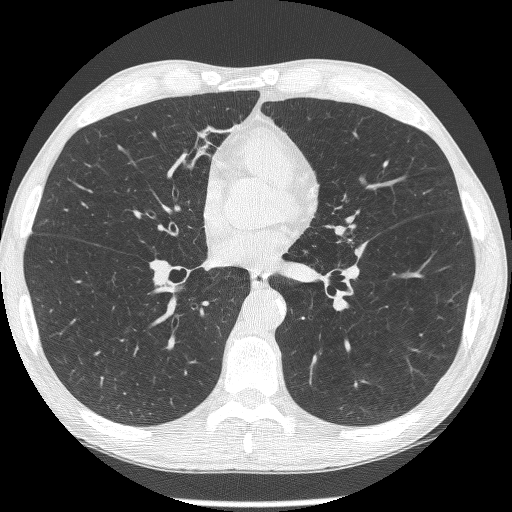
Axial slice from a low-dose chest CT screening exam, second annual screen, lung window (W 1500 / L -600 HU), 1.25 mm slice thickness, 120 kVp, slice 129 of 293 in the series. Male participant, aged 62 years at enrolment. Former smoker at enrolment.
Expert-annotated lung lesion, box from (x=322, y=216) to (x=370, y=264) px. The screening reader recorded 2 non-calcified nodules or masses ≥4 mm on this exam (lingula, lingula); which of them this box marks is not recorded. Participant outcome: lung cancer diagnosed 95 days after this screen — small cell carcinoma, NOS, left upper lobe, stage IIIA (AJCC 6th edition).